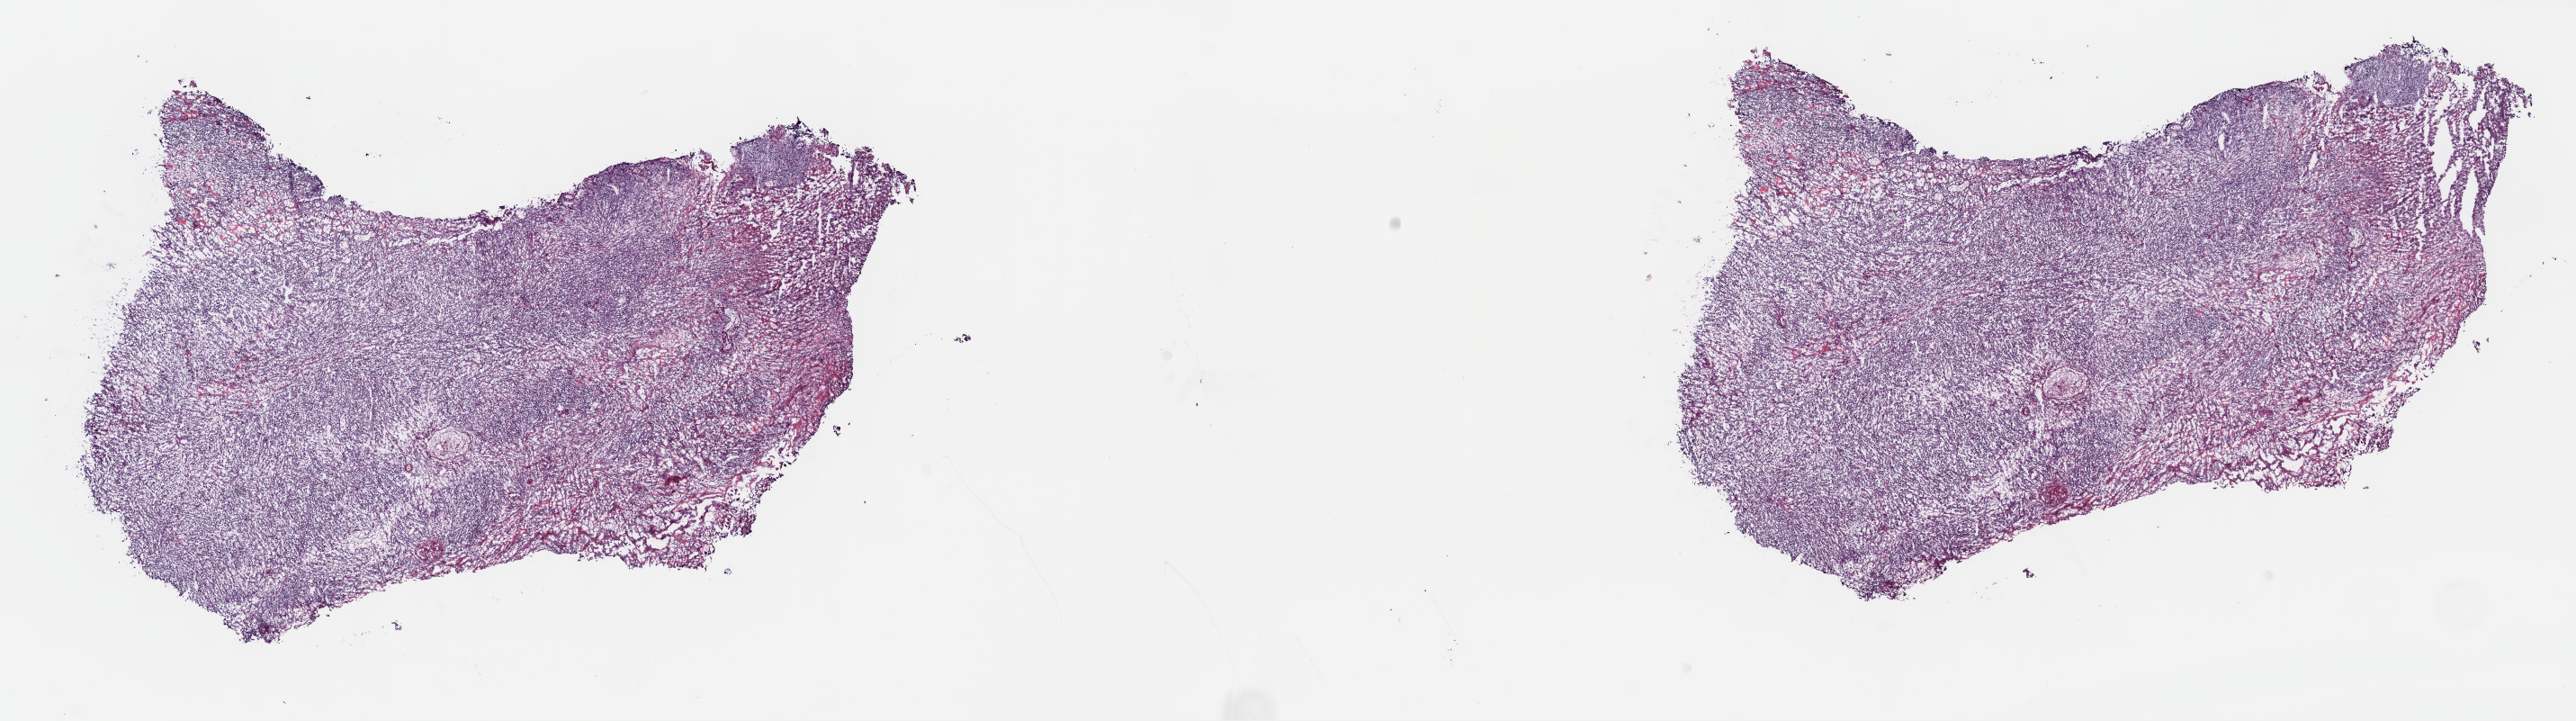
Whole-slide histology image, H&E, shown as a low-resolution overview of the whole scanned area (about 23.2 x 6.5 mm); frozen section; lymphoid tissue, primary tumour sample. Female, age 27 years at initial diagnosis. Slide review estimates, as recorded: tumour cells 80%, tumour nuclei 90%.
Histologic diagnosis: Diffuse large B-cell lymphoma, NOS.